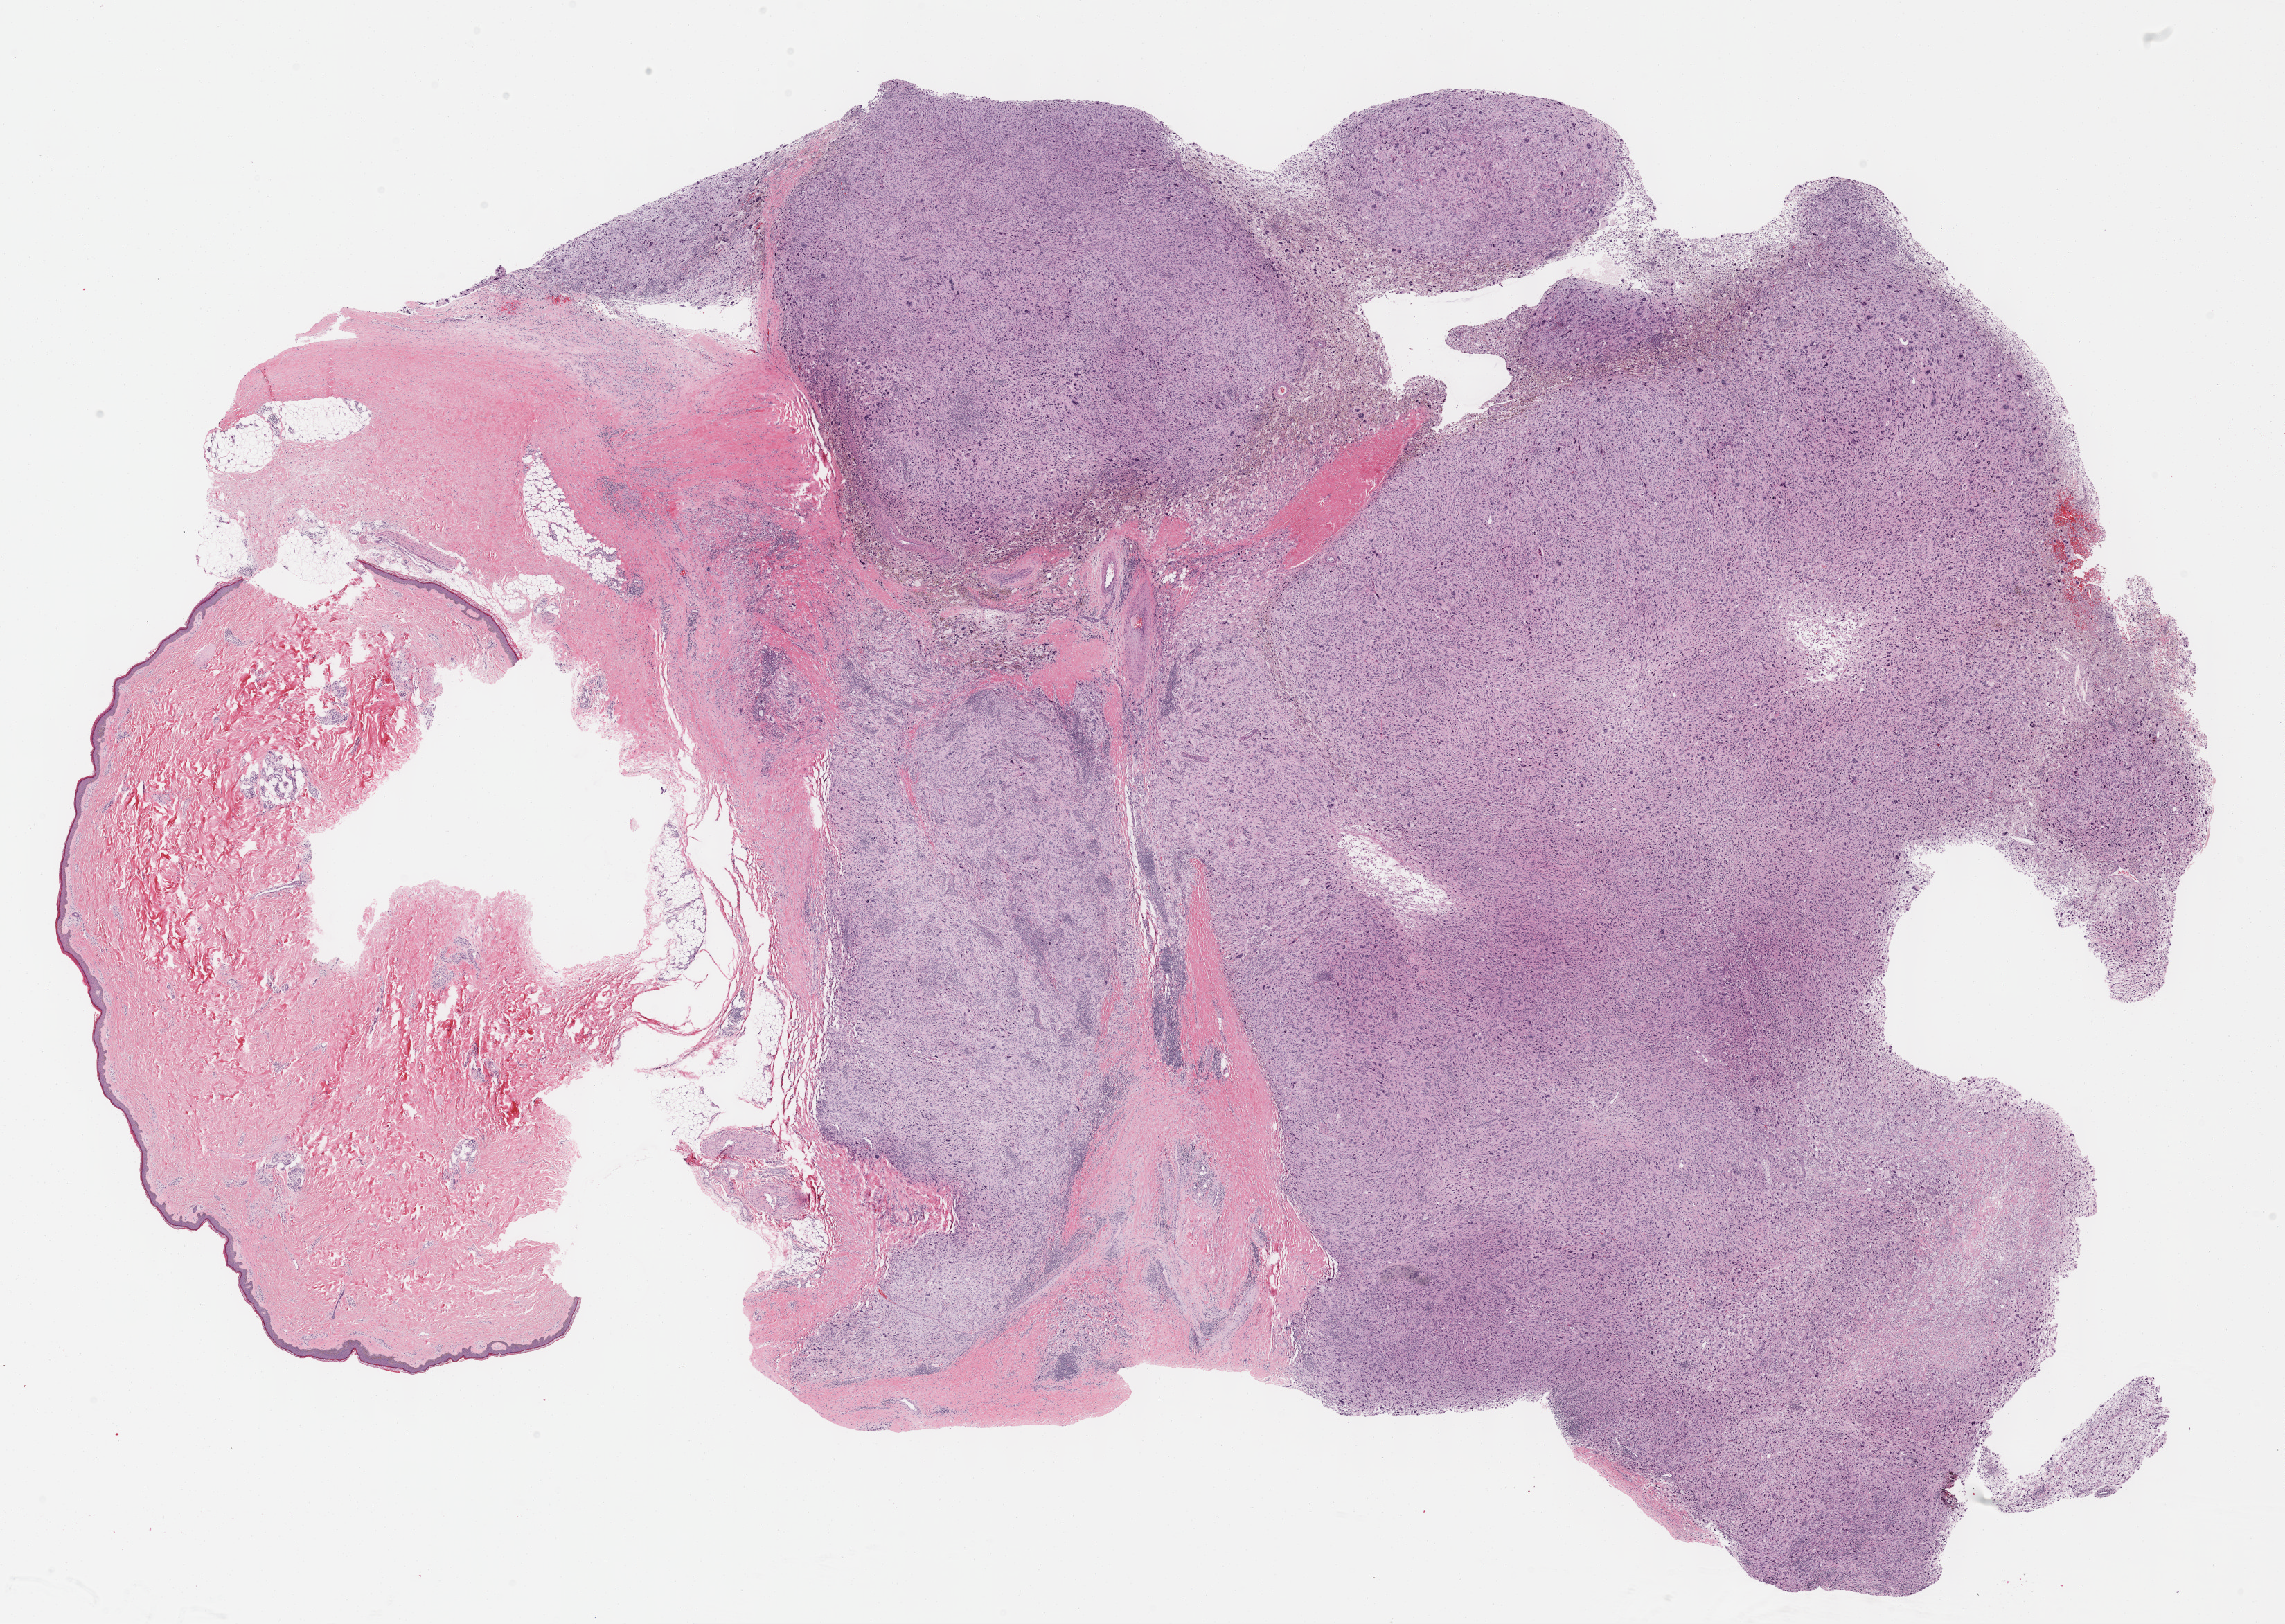
H&E-stained whole-slide image — shown as a low-resolution overview of the whole scanned area (about 26.7 x 18.9 mm), FFPE section, primary tumour sample from the connective, subcutaneous and other soft tissues. Female, age 67 years at initial diagnosis.
Histologic diagnosis: Undifferentiated sarcoma (connective, subcutaneous and other soft tissues of lower limb and hip).